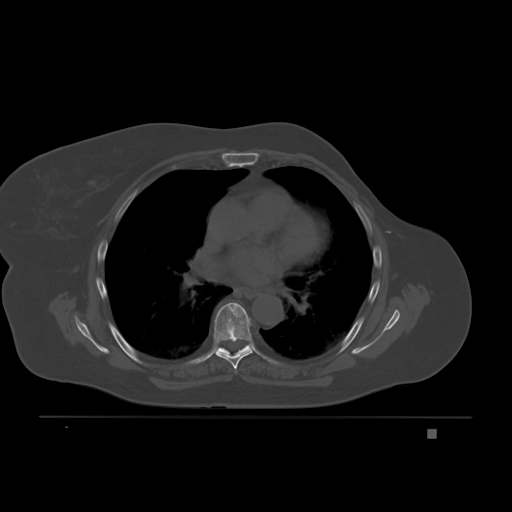
CT including the spine, one axial slice; position 134 of 221 along the scan axis; bone window (W 1800 / L 400 HU); 3 mm slice thickness; 512 × 512 image matrix. Female patient, age 63 years. Case-level facts recorded for this patient, not image findings: primary cancer: breast.
Annotated regions visible in this slice (semi-automatically segmented with operator editing):
- T6 vertebra: bounding box [x1, y1, x2, y2] px = [214, 302, 252, 372]
- T7 vertebra: [218, 345, 248, 354]